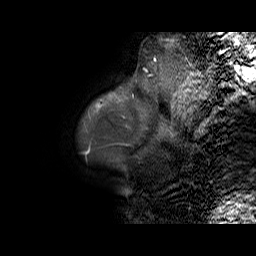
Breast MRI (dynamic contrast-enhanced), one sagittal slice; position 5 of 70 along the scan axis; dynamic contrast-enhanced series, time point 2 of 6 at this slice position (early post-contrast); 1.5 T; TE 5.5 ms, TR 32.9 ms; 256 × 256 image matrix, field of view 240 × 240 mm. Female patient. From the clinical record (not read from this slice): setting: breast cancer imaged before/during neoadjuvant chemotherapy; receptor status: HER2-positive.
Annotated regions visible in this slice (semi-automatically segmented with operator editing):
- analysis volume of interest (the breast-tissue region the enhancement analysis was run in; not a lesion): bounding box <96,84,140,112> (left, top, right, bottom; pixels)
- tumour enhancement mask (voxels above the 100 % enhancement threshold inside the analysis volume of interest): <98,105,100,107>